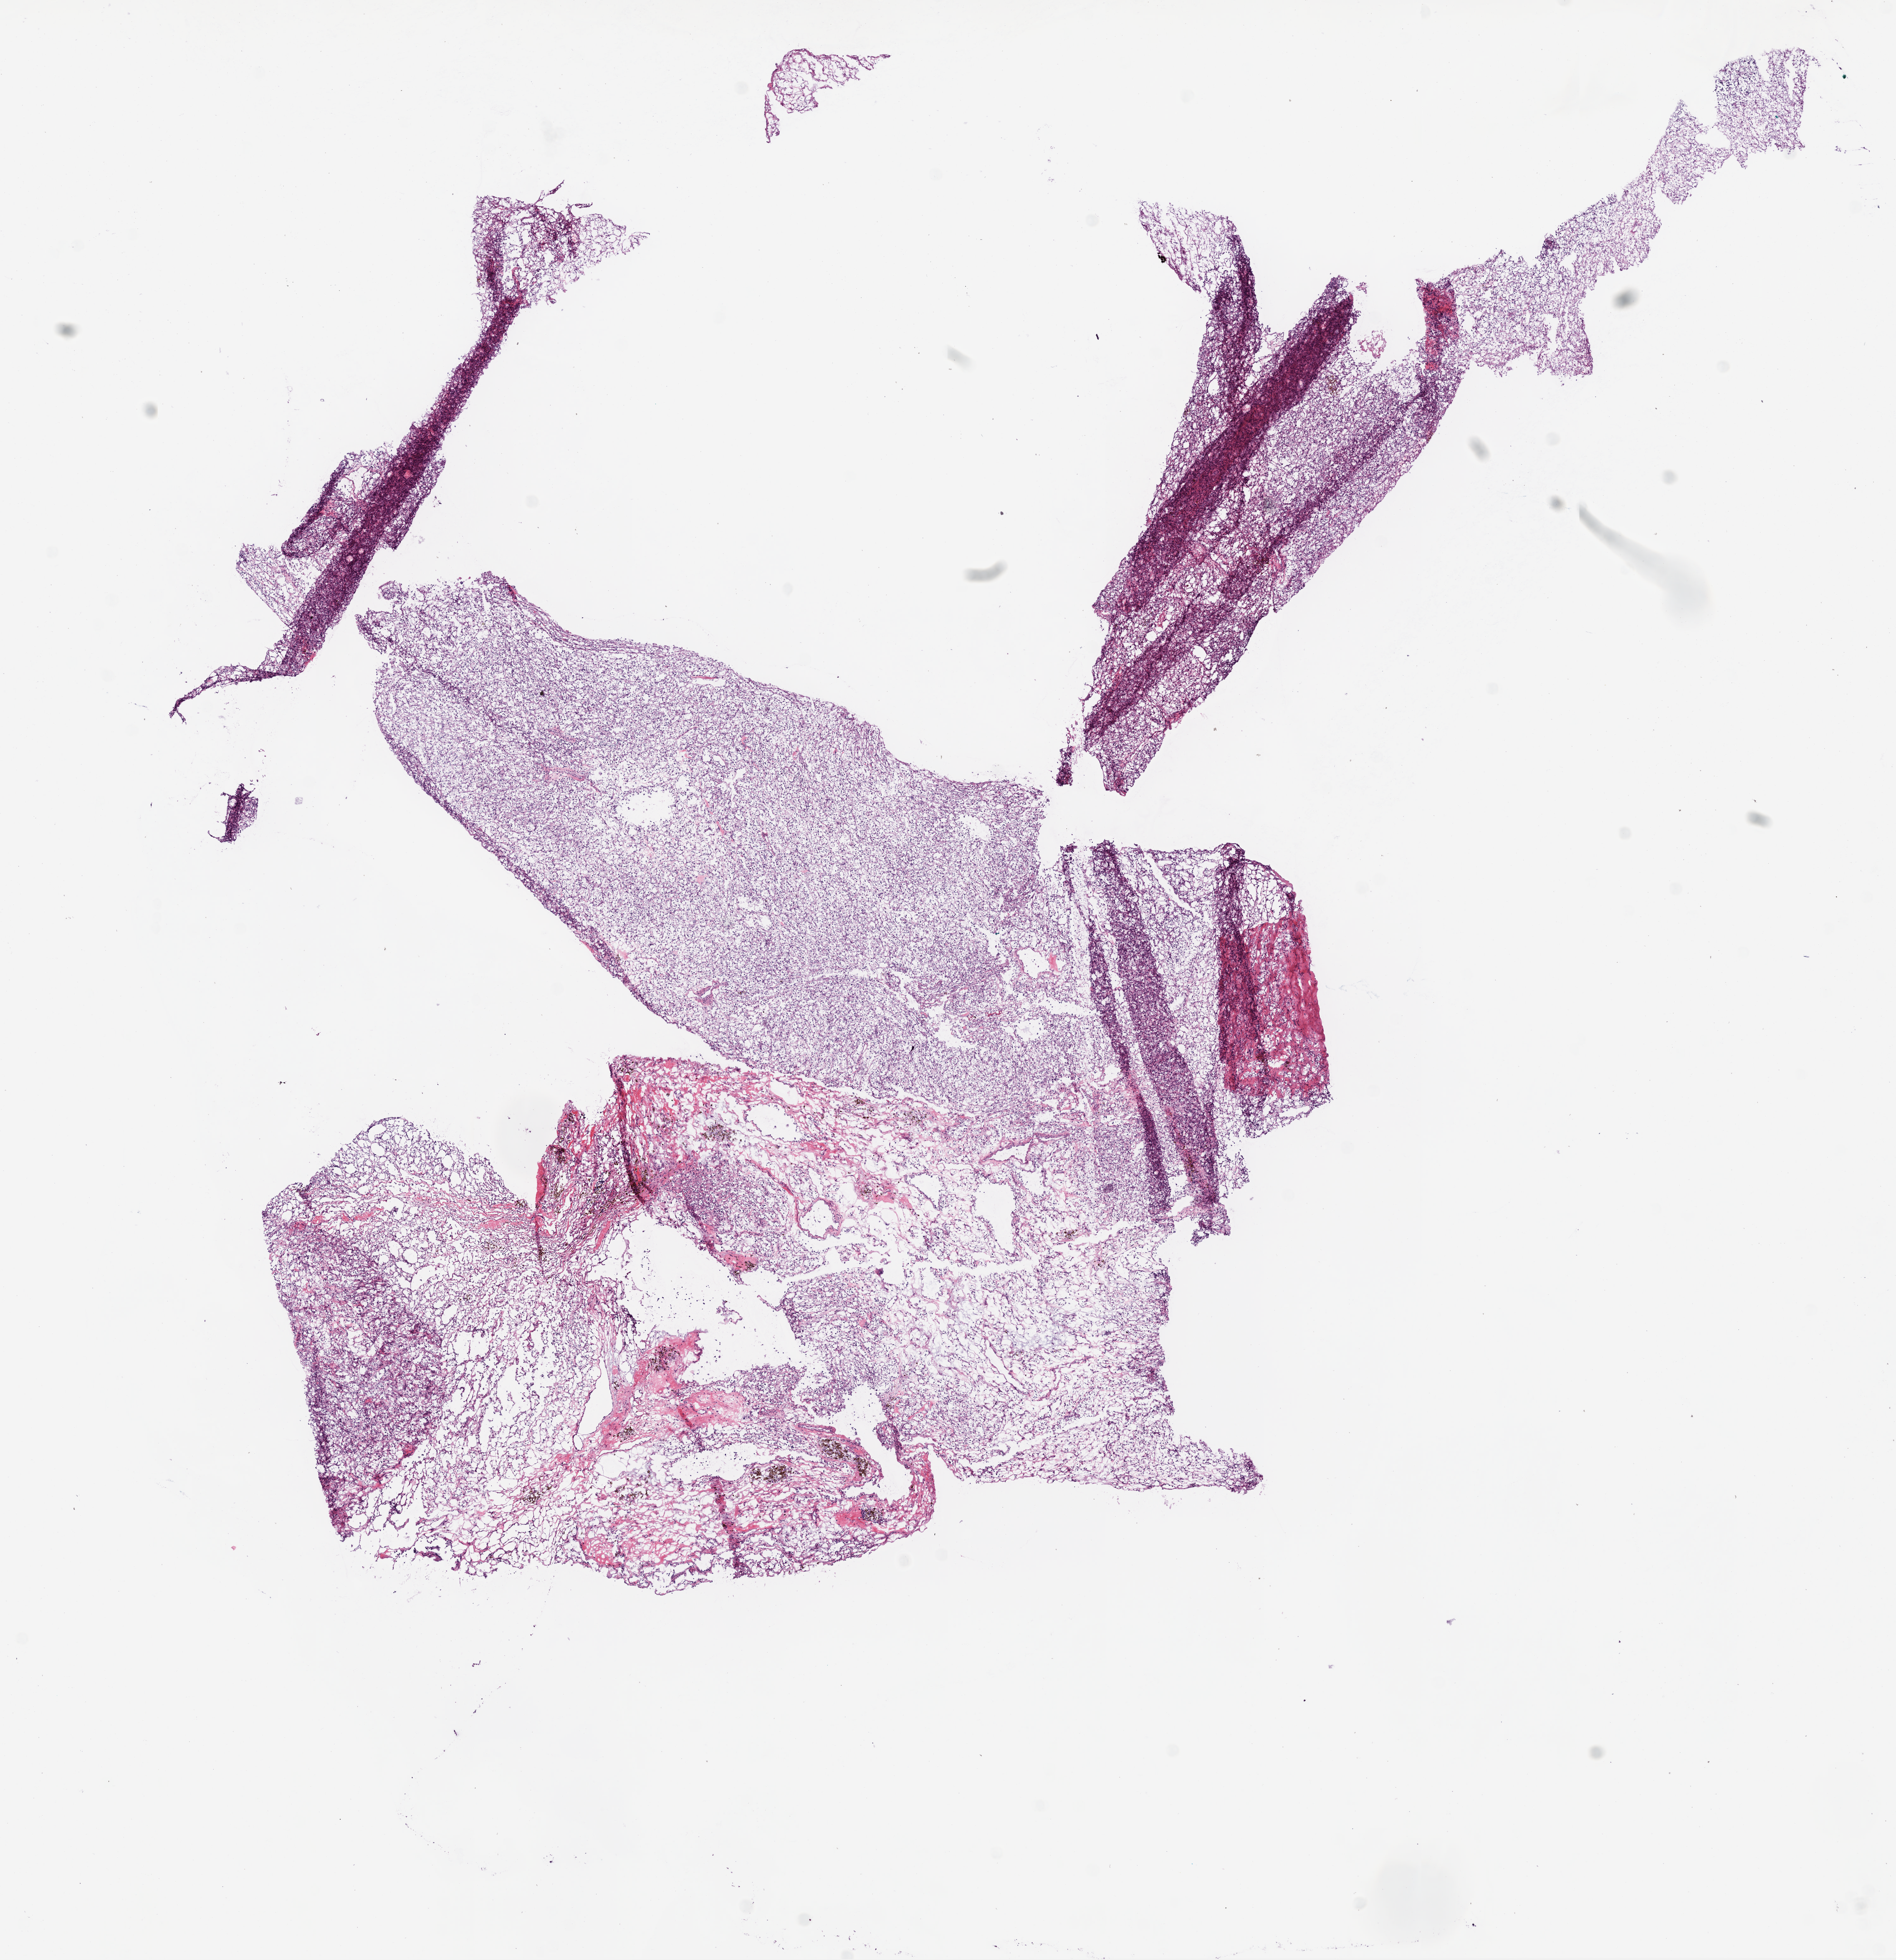
Whole-slide histology image, H&E — low-resolution overview of the scanned area, about 12.0 x 12.4 mm (slide scanned at 20x); frozen section; sample: primary tumour, kidney. Male patient; age at initial diagnosis 58 years. Slide review estimates, as recorded: tumour cells 95%, tumour nuclei 70%.
Pathologic diagnosis: Clear cell adenocarcinoma, NOS.